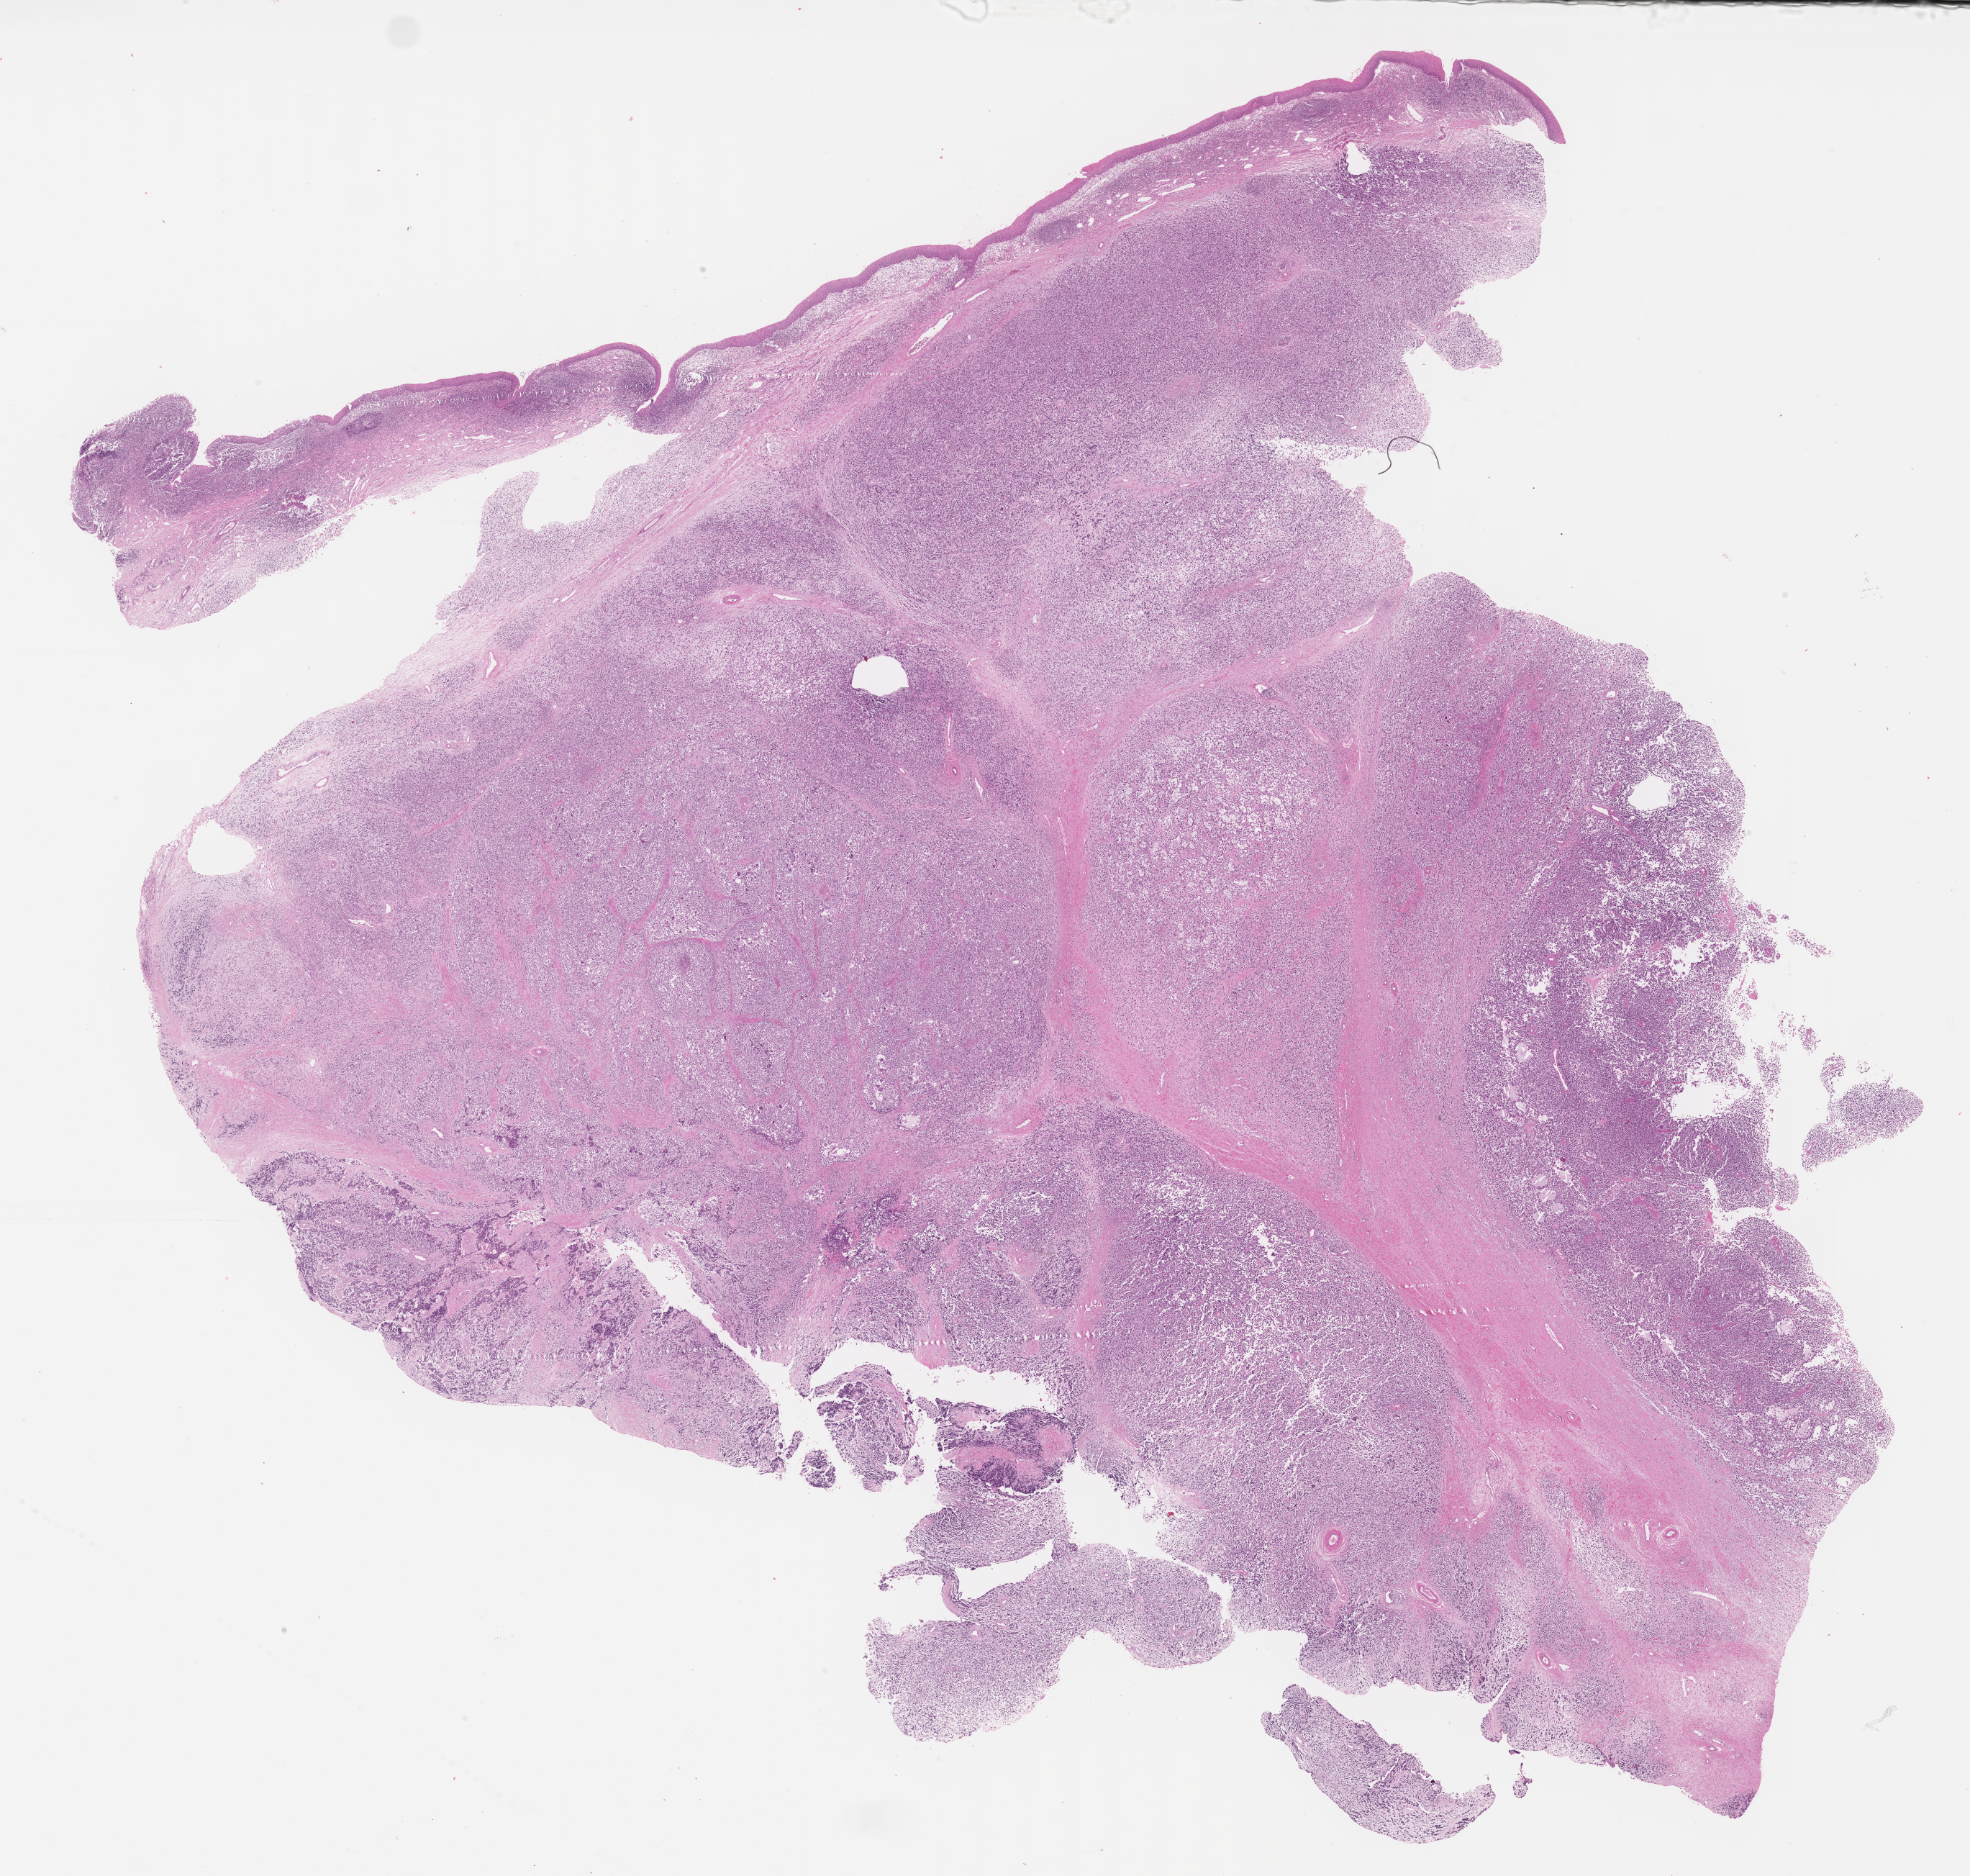
Whole-slide image, H&E stain of tumor tissue, shown as a low-resolution overview of the whole scanned area (about 22.1 x 21.1 mm), FFPE section. Patient: male, age 10.2 years at diagnosis.
Diagnosis: rhabdomyosarcoma; histological classification: embryonal rhabdomyosarcoma.